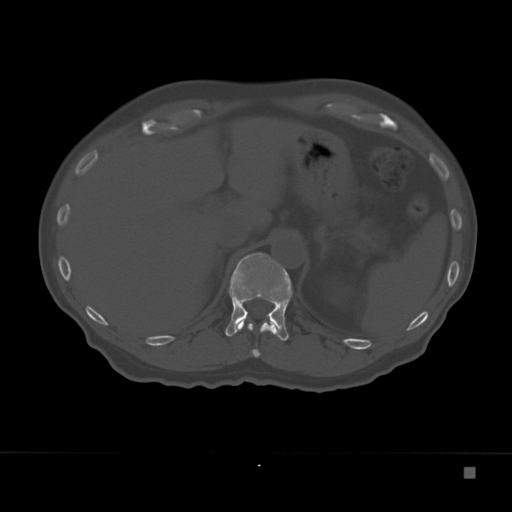
CT including the spine, one axial slice; slice 140 of 332 in the series (ordered by position); 120 kVp; bone window (W 1800 / L 400 HU); 1.5 mm slice thickness; 512 × 512 image matrix, field of view 389 × 389 mm. Male patient, age 72 years. From the clinical record (not read from this slice): primary cancer: skeletal.
Structures marked on this image (semi-automatic segmentation, software-assisted and operator-edited):
- T11 vertebra: bounding box <237,320,278,358> (left, top, right, bottom; pixels)
- T12 vertebra: <225,252,292,341>